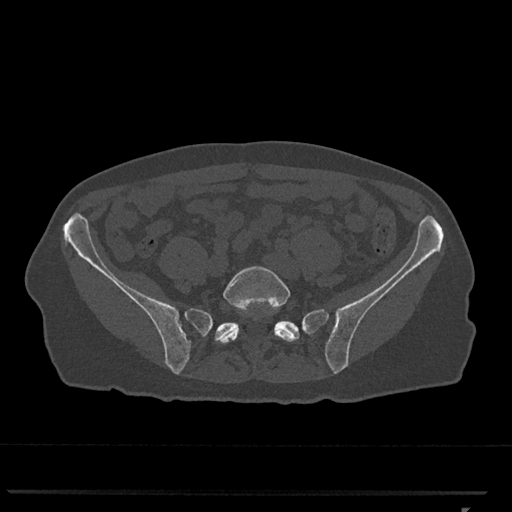
CT including the spine, one axial slice; slice 129 of 793 in the series (ordered by position); reconstruction kernel Br40s/3; 120 kVp; bone window (W 1800 / L 400 HU); 512 × 512 image matrix, field of view 380 × 380 mm. Patient: female, 62 years. From the clinical record (not read from this slice): primary cancer: renal.
Annotated regions visible in this slice (semi-automatically segmented with operator editing):
- L5 vertebra: bounding box [x1, y1, x2, y2] px = [218, 266, 297, 344]